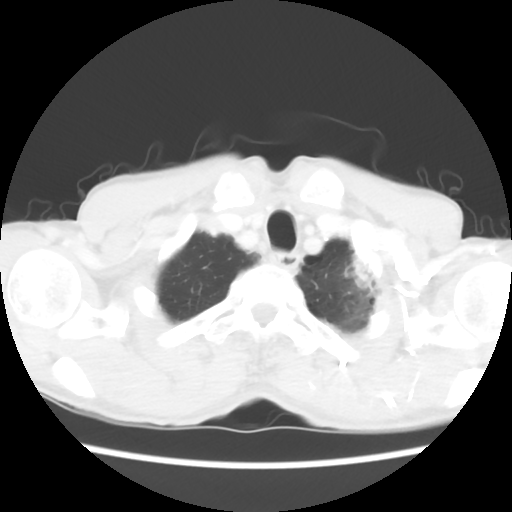
Chest CT, one axial slice; position 55 of 60 along the scan axis; lung window (W 1500 / L -600 HU); 512 × 512 image matrix. Male patient, age 64 years. Case-level facts recorded for this patient, not image findings: clinical TNM (as recorded): T3 N3 M0.
Annotated regions visible in this slice (rectangle marked by the reading radiologist):
- lung tumour (recorded histology: adenocarcinoma): bounding box [x1, y1, x2, y2] px = [342, 255, 372, 294]